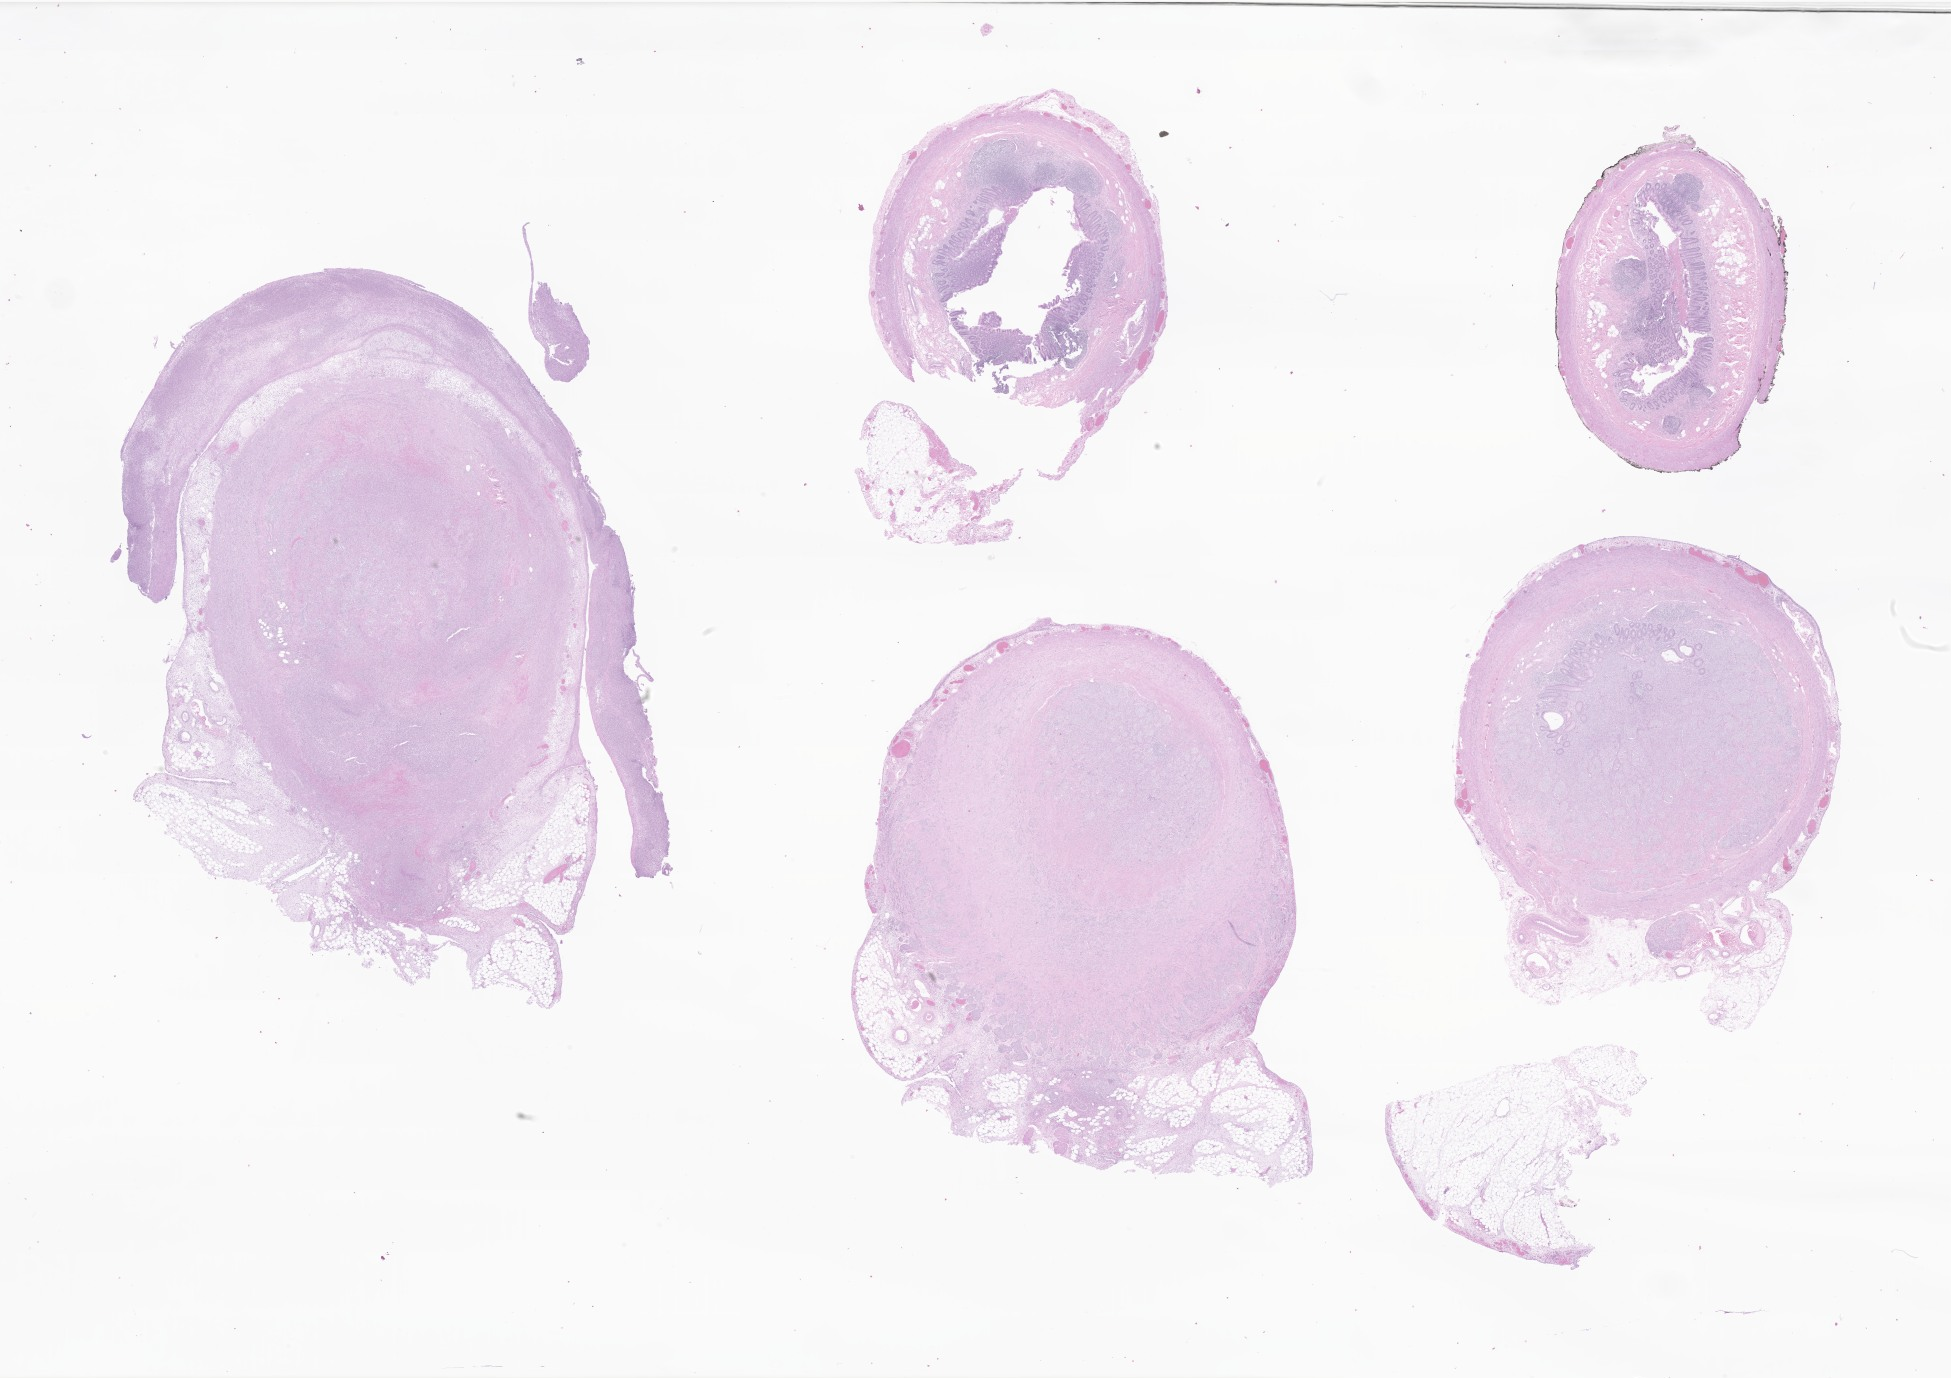
Digitized hematoxylin and eosin (H&E)-stained section of tumor tissue from the appendix, low-resolution overview of the scanned area, about 32.9 x 23.2 mm, formalin-fixed, paraffin-embedded (FFPE) tissue. Patient female; age 191 months (15 years 11 months).
Recorded diagnosis: Neuroendocrine carcinoma, NOS.